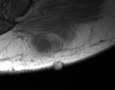
MRI of an extremity soft-tissue mass, one axial slice; position 13 of 35 along the scan axis; MR volume resampled by the dataset authors to the PET/CT grid (not the native acquisition matrix); 115 × 90 image matrix. Male patient. From the clinical record (not read from this slice): histological type: pleiomorphic leiomyosarcoma; grade: high; site of the primary tumour: left buttock.
Annotated regions visible in this slice (expert contour drawn on MRI and transferred to this co-registered scan by the dataset authors):
- gross tumour volume including surrounding oedema: box from (x=30, y=26) to (x=77, y=56) px
- gross tumour volume (mass): (x=35, y=28)–(x=75, y=54)